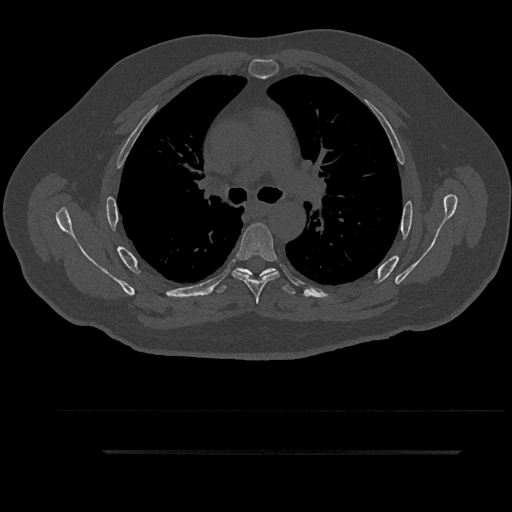
CT including the spine, one axial slice. Position 617 of 797 along the scan axis. 120 kVp. Bone window (W 1800 / L 400 HU). 0.5 mm slice thickness. 512 × 512 image matrix, field of view 432 × 432 mm. Patient: male, 63 years. Case-level facts recorded for this patient, not image findings: primary cancer: renal; vertebrae with lytic lesions (as recorded): T8.
Structures marked on this image (semi-automatic segmentation, software-assisted and operator-edited):
- T5 vertebra: box from (x=232, y=223) to (x=279, y=304) px
- T6 vertebra: (x=215, y=268)–(x=296, y=294)